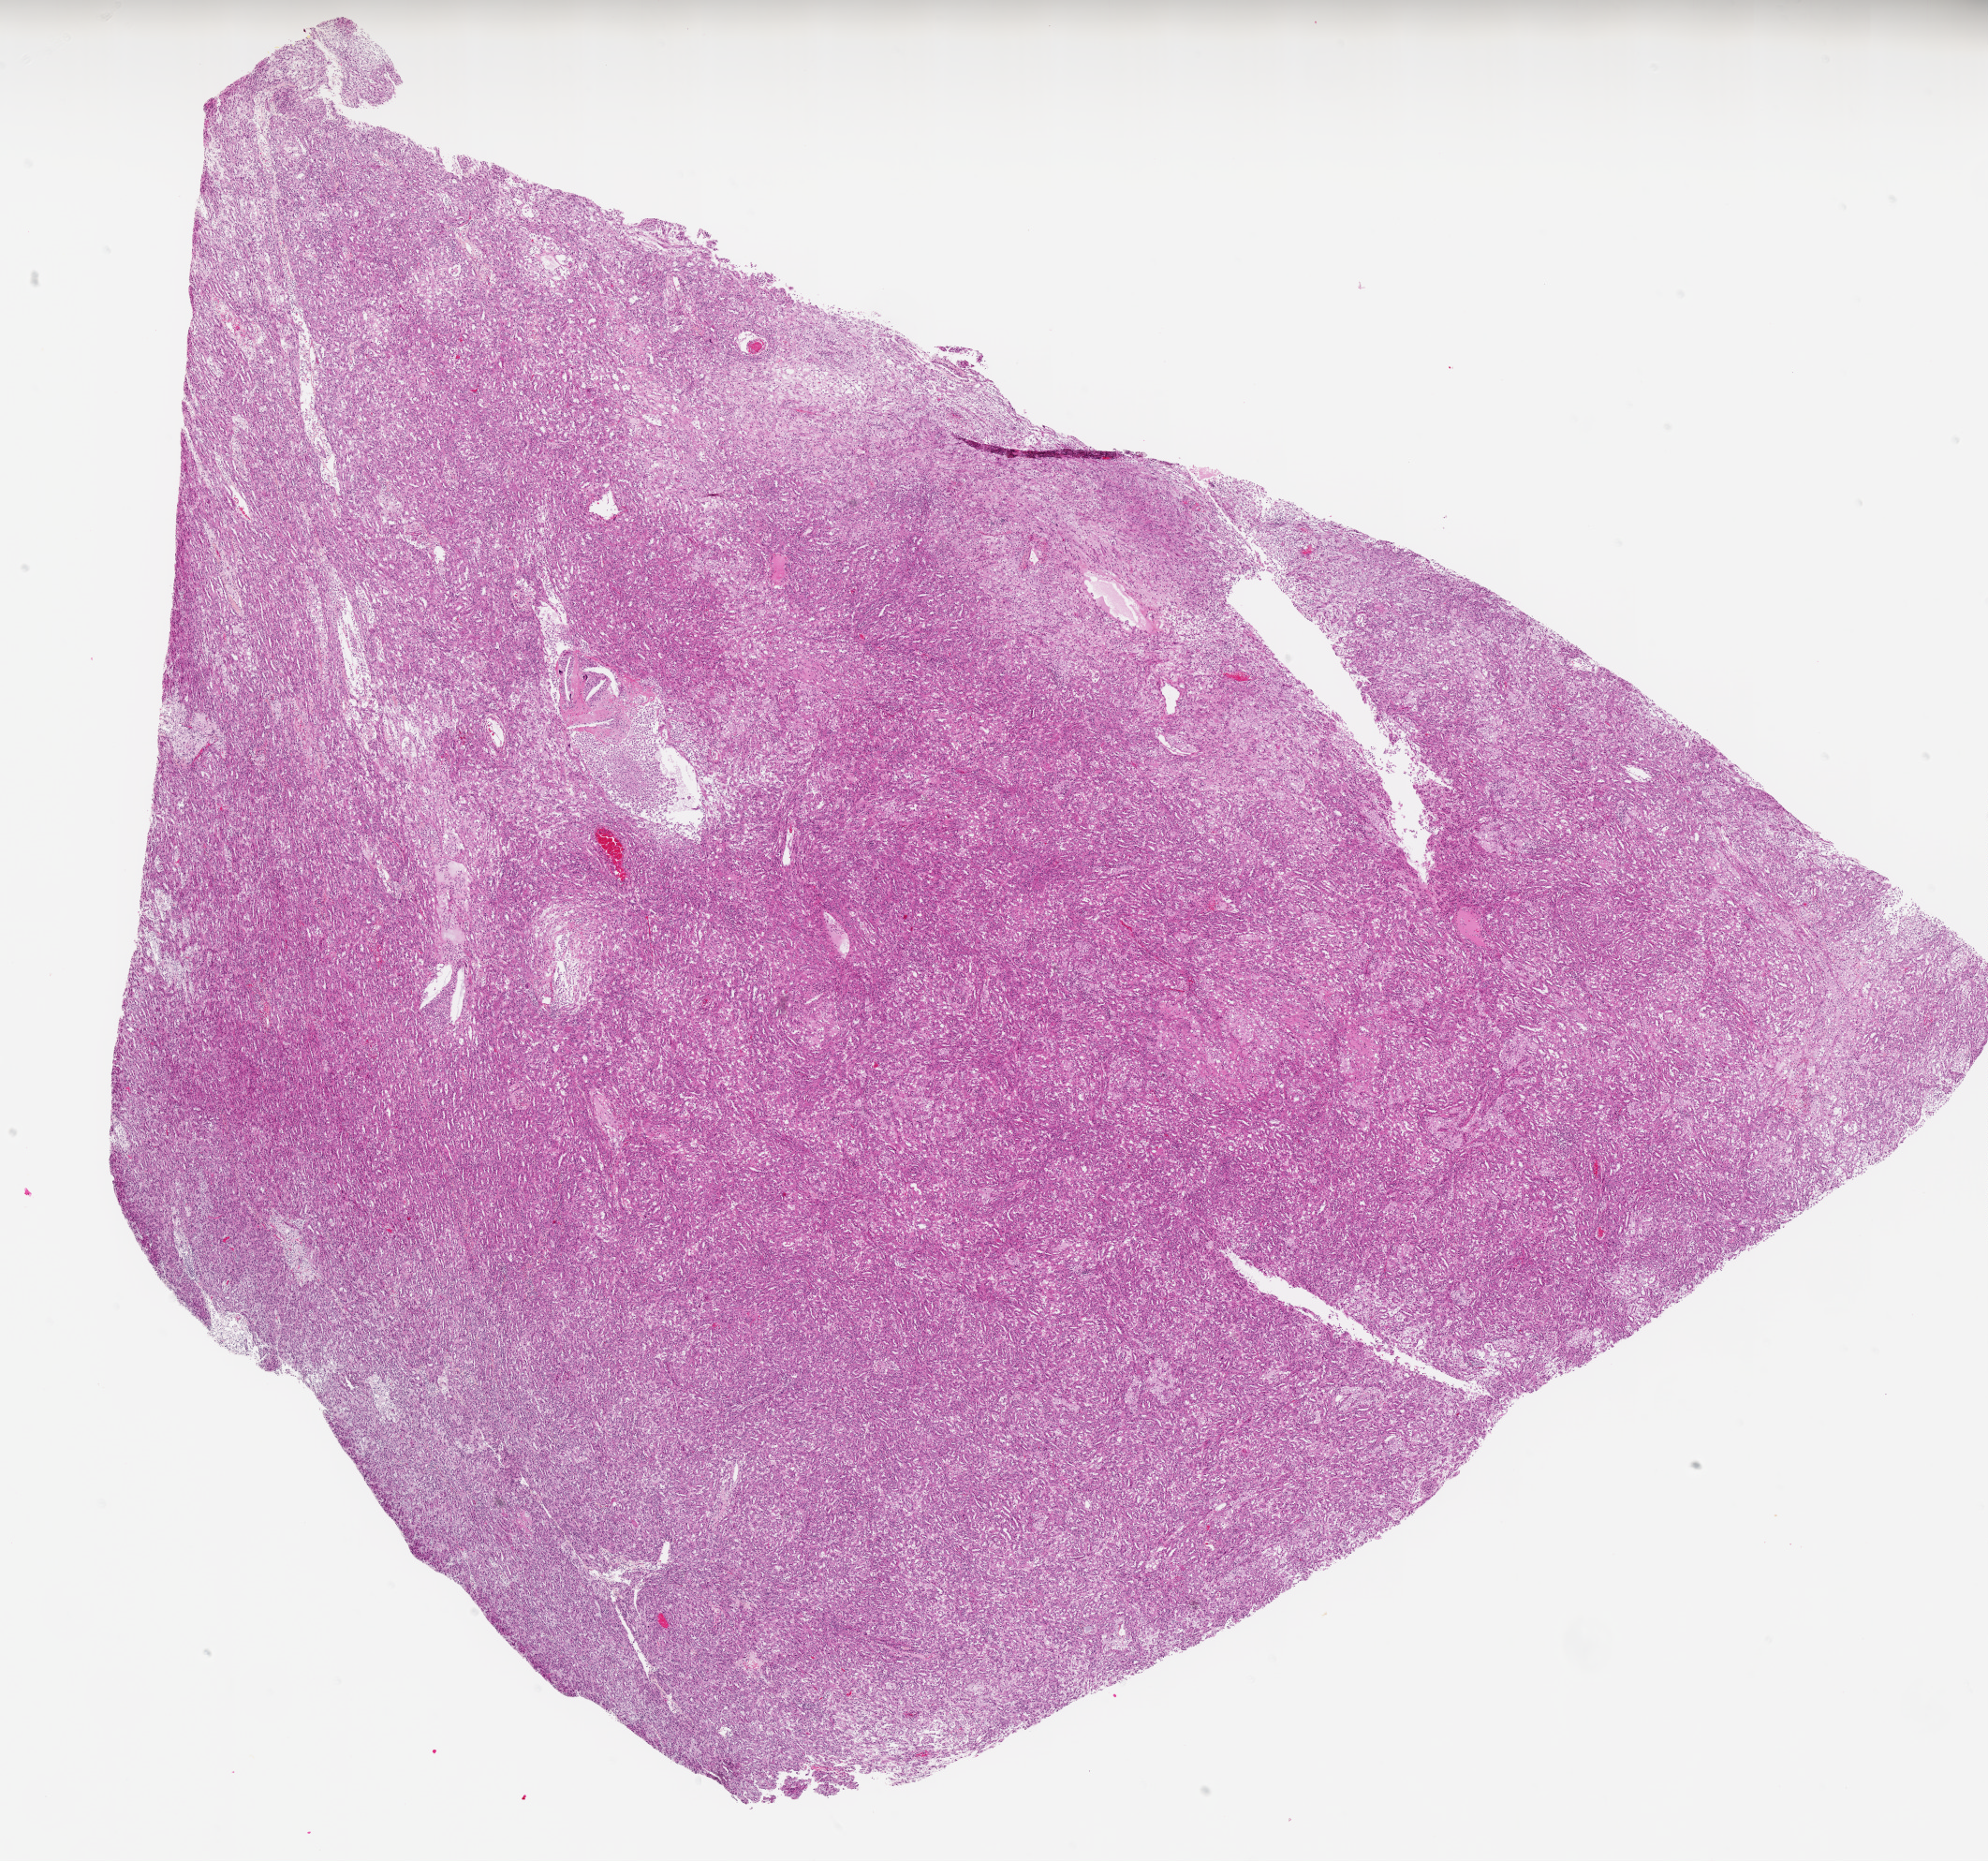
Hematoxylin and eosin (H&E) stained whole-slide image, a low-resolution overview of the entire scanned area, about 17.0 x 15.9 mm (slide scanned at 20x), formalin-fixed paraffin-embedded (FFPE) diagnostic section, primary tumour sample from the kidney. Male, age 82 years at initial diagnosis.
Pathologic diagnosis: Papillary adenocarcinoma, NOS.